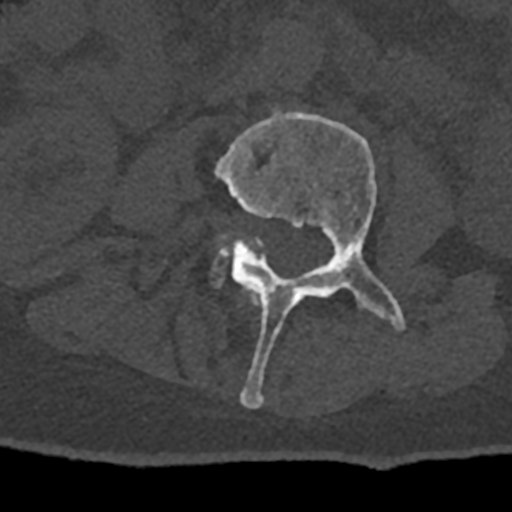
CT including the spine, one axial slice. Position 313 of 797 along the scan axis. Reconstruction kernel Br40s/3. 120 kVp. Bone window (W 1800 / L 400 HU). 0.5 mm slice thickness. 512 × 512 image matrix, field of view 160 × 160 mm. Patient: male, 74 years. Case-level facts recorded for this patient, not image findings: primary cancer: renal.
Outlined on this slice (semi-automatically segmented with operator editing):
- L2 vertebra: box from (x=253, y=298) to (x=258, y=304) px
- L3 vertebra: (x=215, y=109)–(x=405, y=408)
- L4 vertebra: (x=212, y=237)–(x=262, y=285)